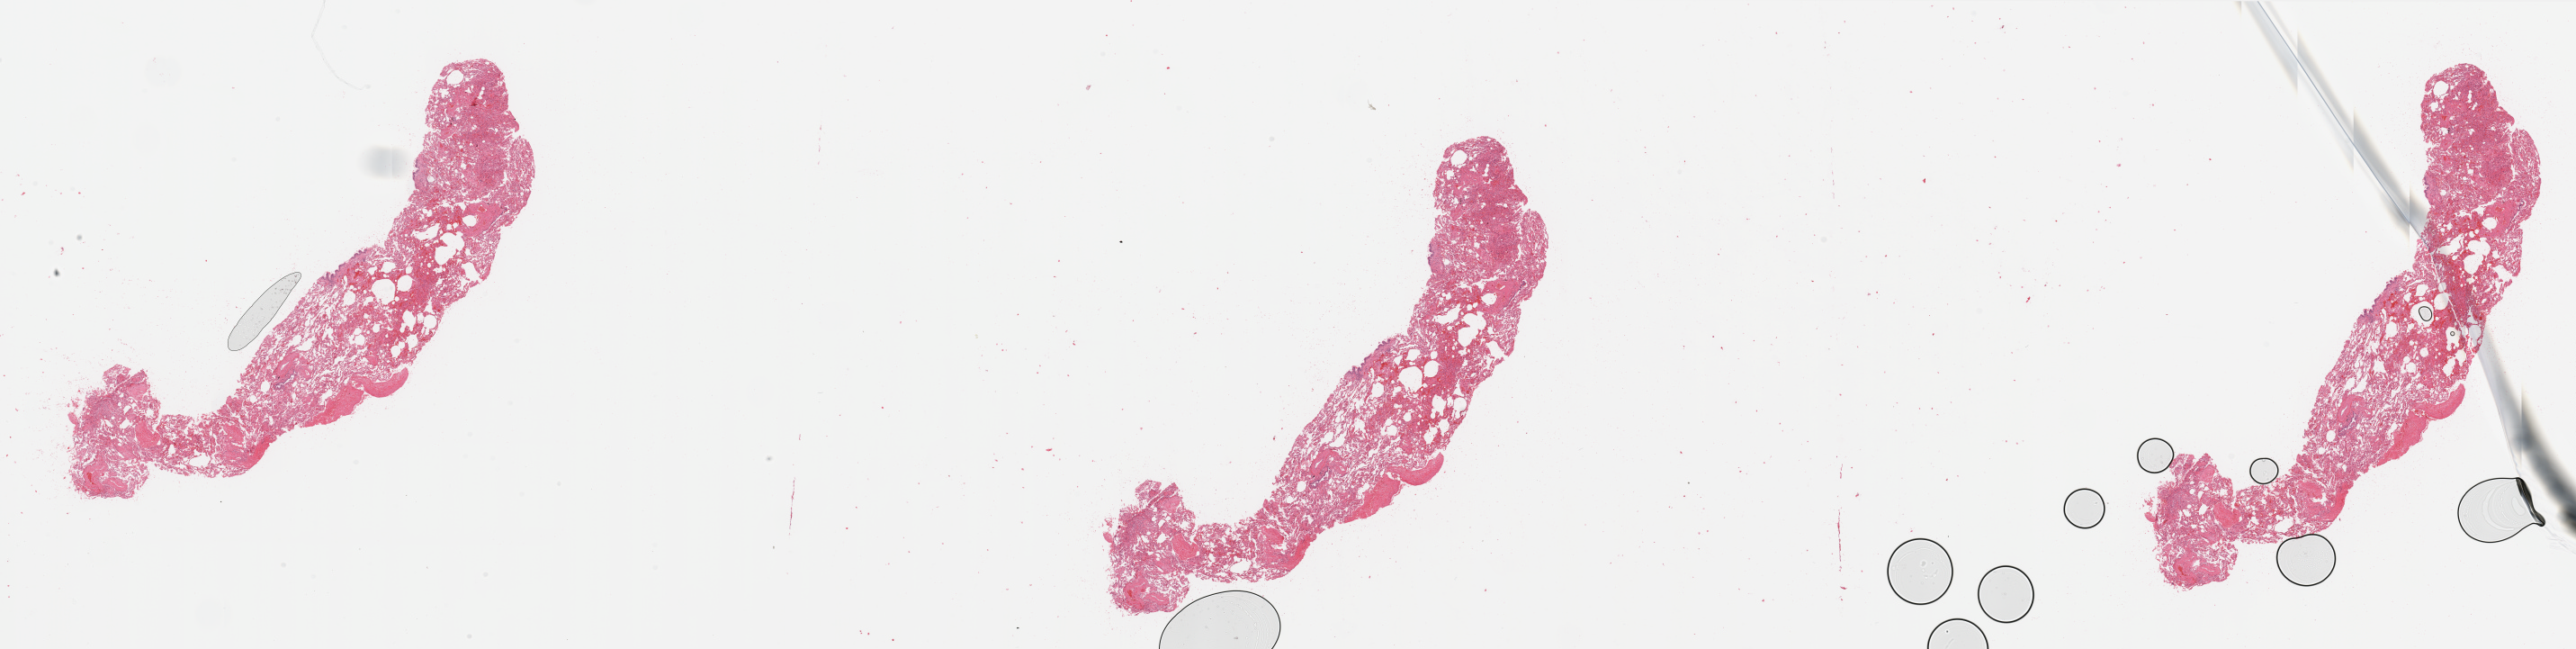
H&E-stained whole-slide image — a low-resolution overview of the entire scanned area, about 45.3 x 11.4 mm. Normal (non-tumour) tissue sample, sampled site: lung. 81-year-old male patient.
This section: normal (non-tumour) tissue from the same patient. Patient diagnosis: Adenocarcinoma, NOS.